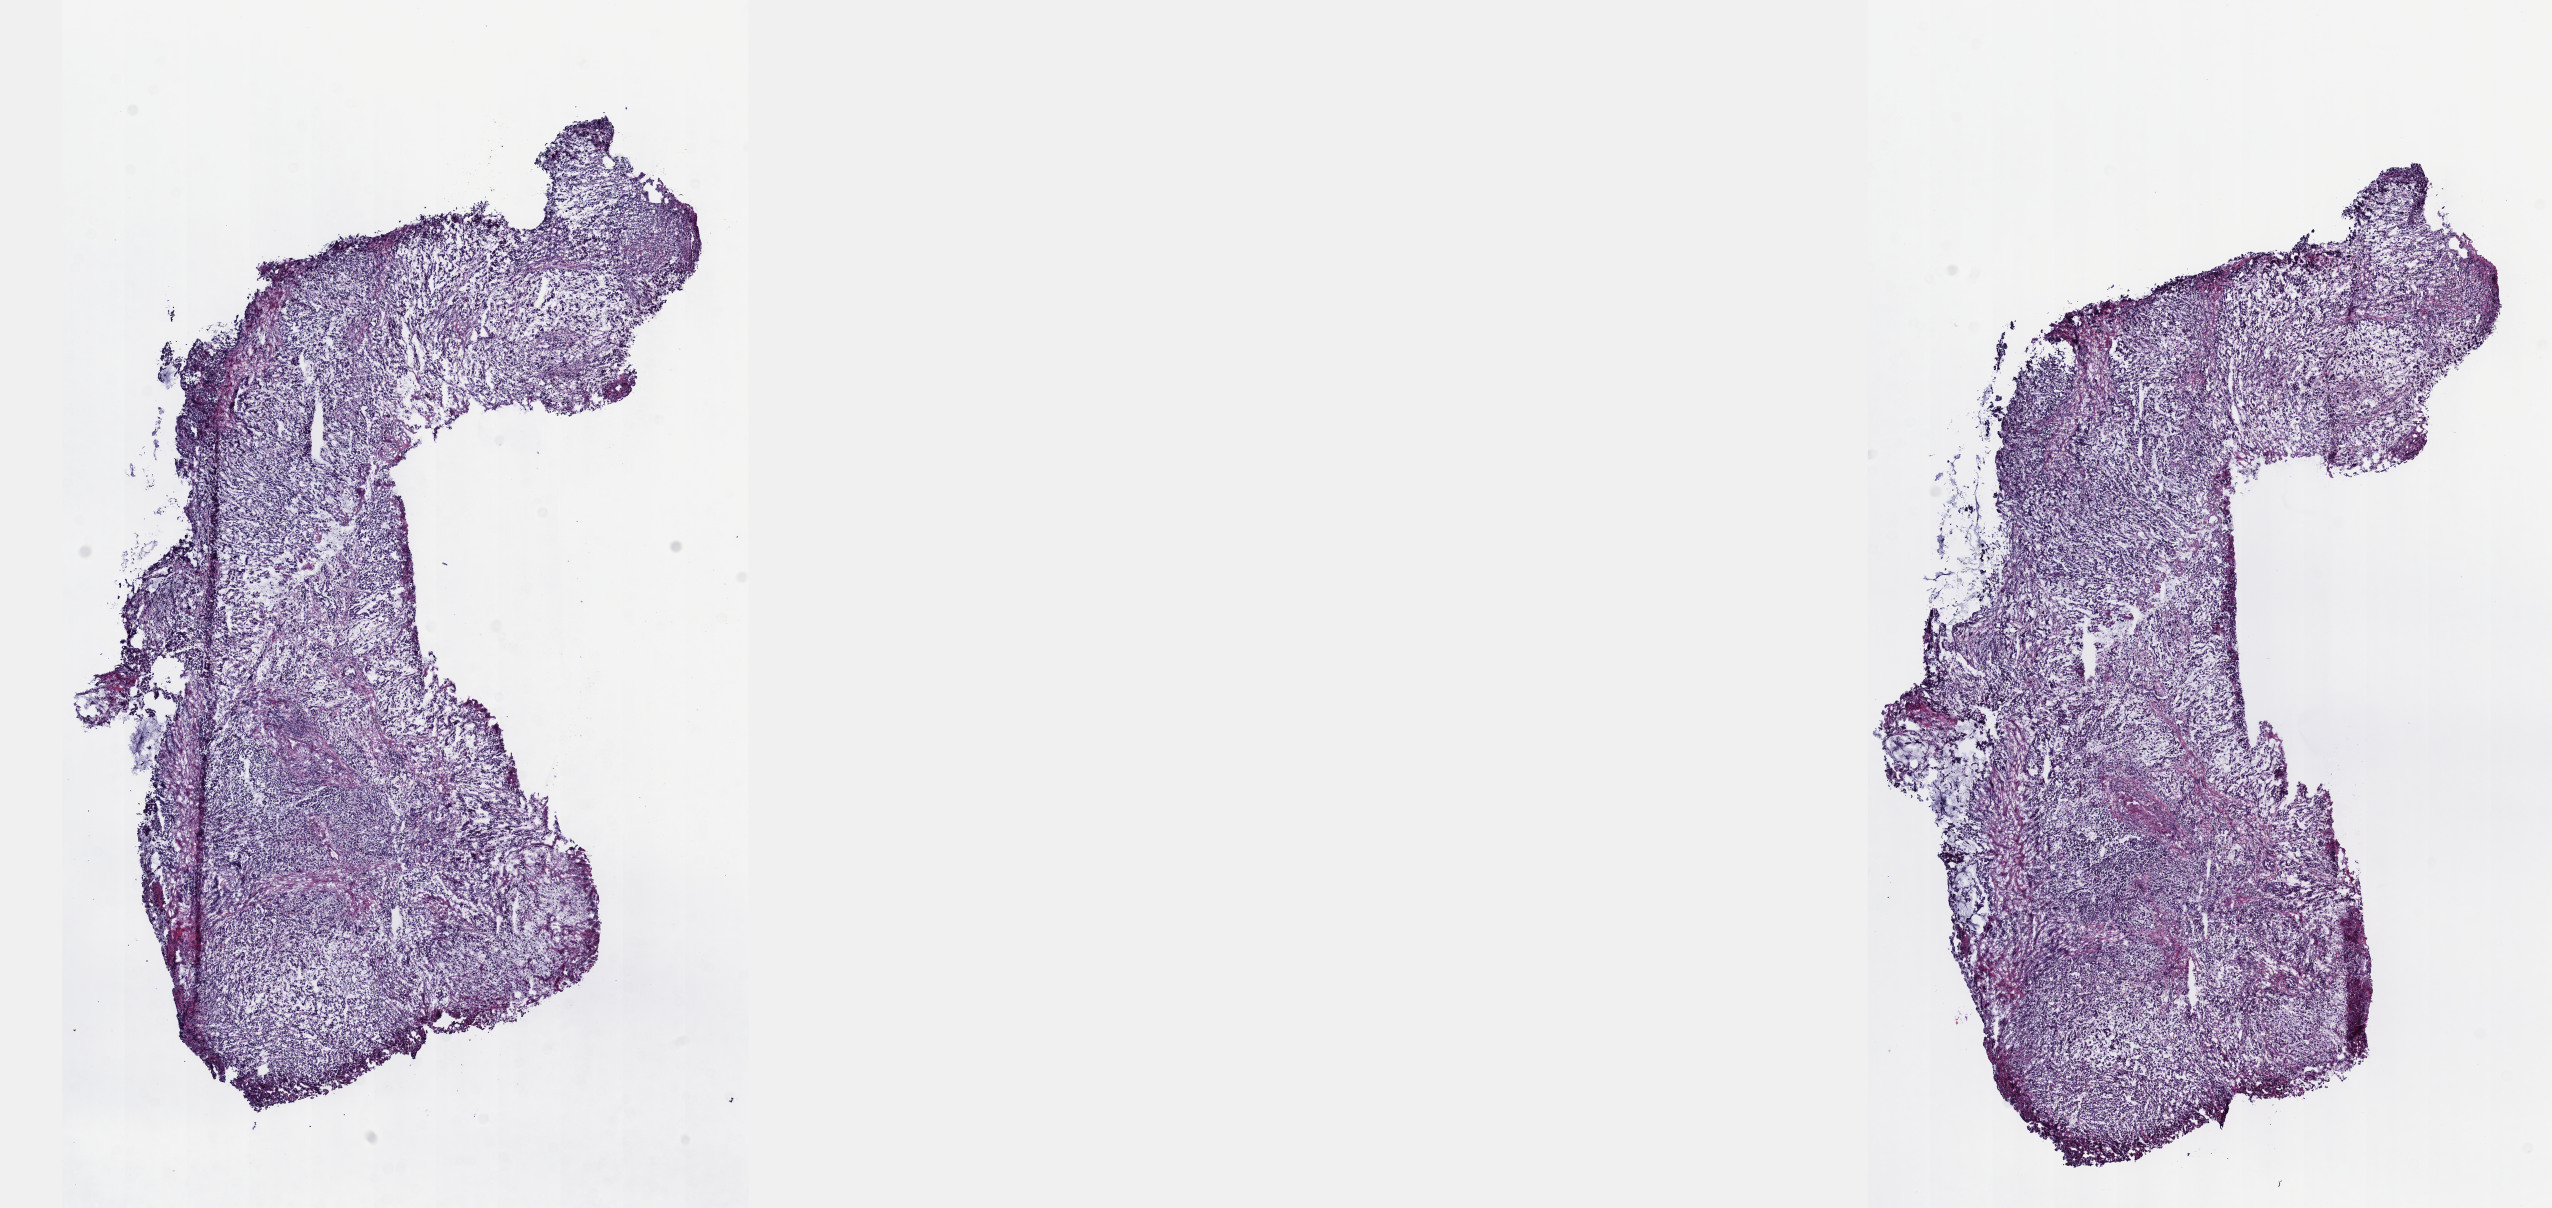
Whole-slide histology image, Hematoxylin and eosin (H&E) stained, shown as a low-resolution overview of the whole scanned area (about 20.6 x 9.8 mm). Frozen section from the top of the tissue portion. Stomach, primary tumour sample. Patient: male, age at initial diagnosis 61 years. Histologic grade: G3 (poorly differentiated). Slide review estimates, as recorded: tumour cells 80%, tumour nuclei 80%, normal cells 0%, stromal cells 20%, necrosis 0%. Inflammatory infiltration, as recorded: lymphocyte infiltration 40%, monocyte infiltration 20%, neutrophil infiltration 20%.
- diagnosis: Tubular adenocarcinoma (cardia, NOS)
- TNM: T3 N3 M0
- lymph nodes positive (case pathology): 25 of 28 examined
- AJCC pathologic stage: IV (6th edition)